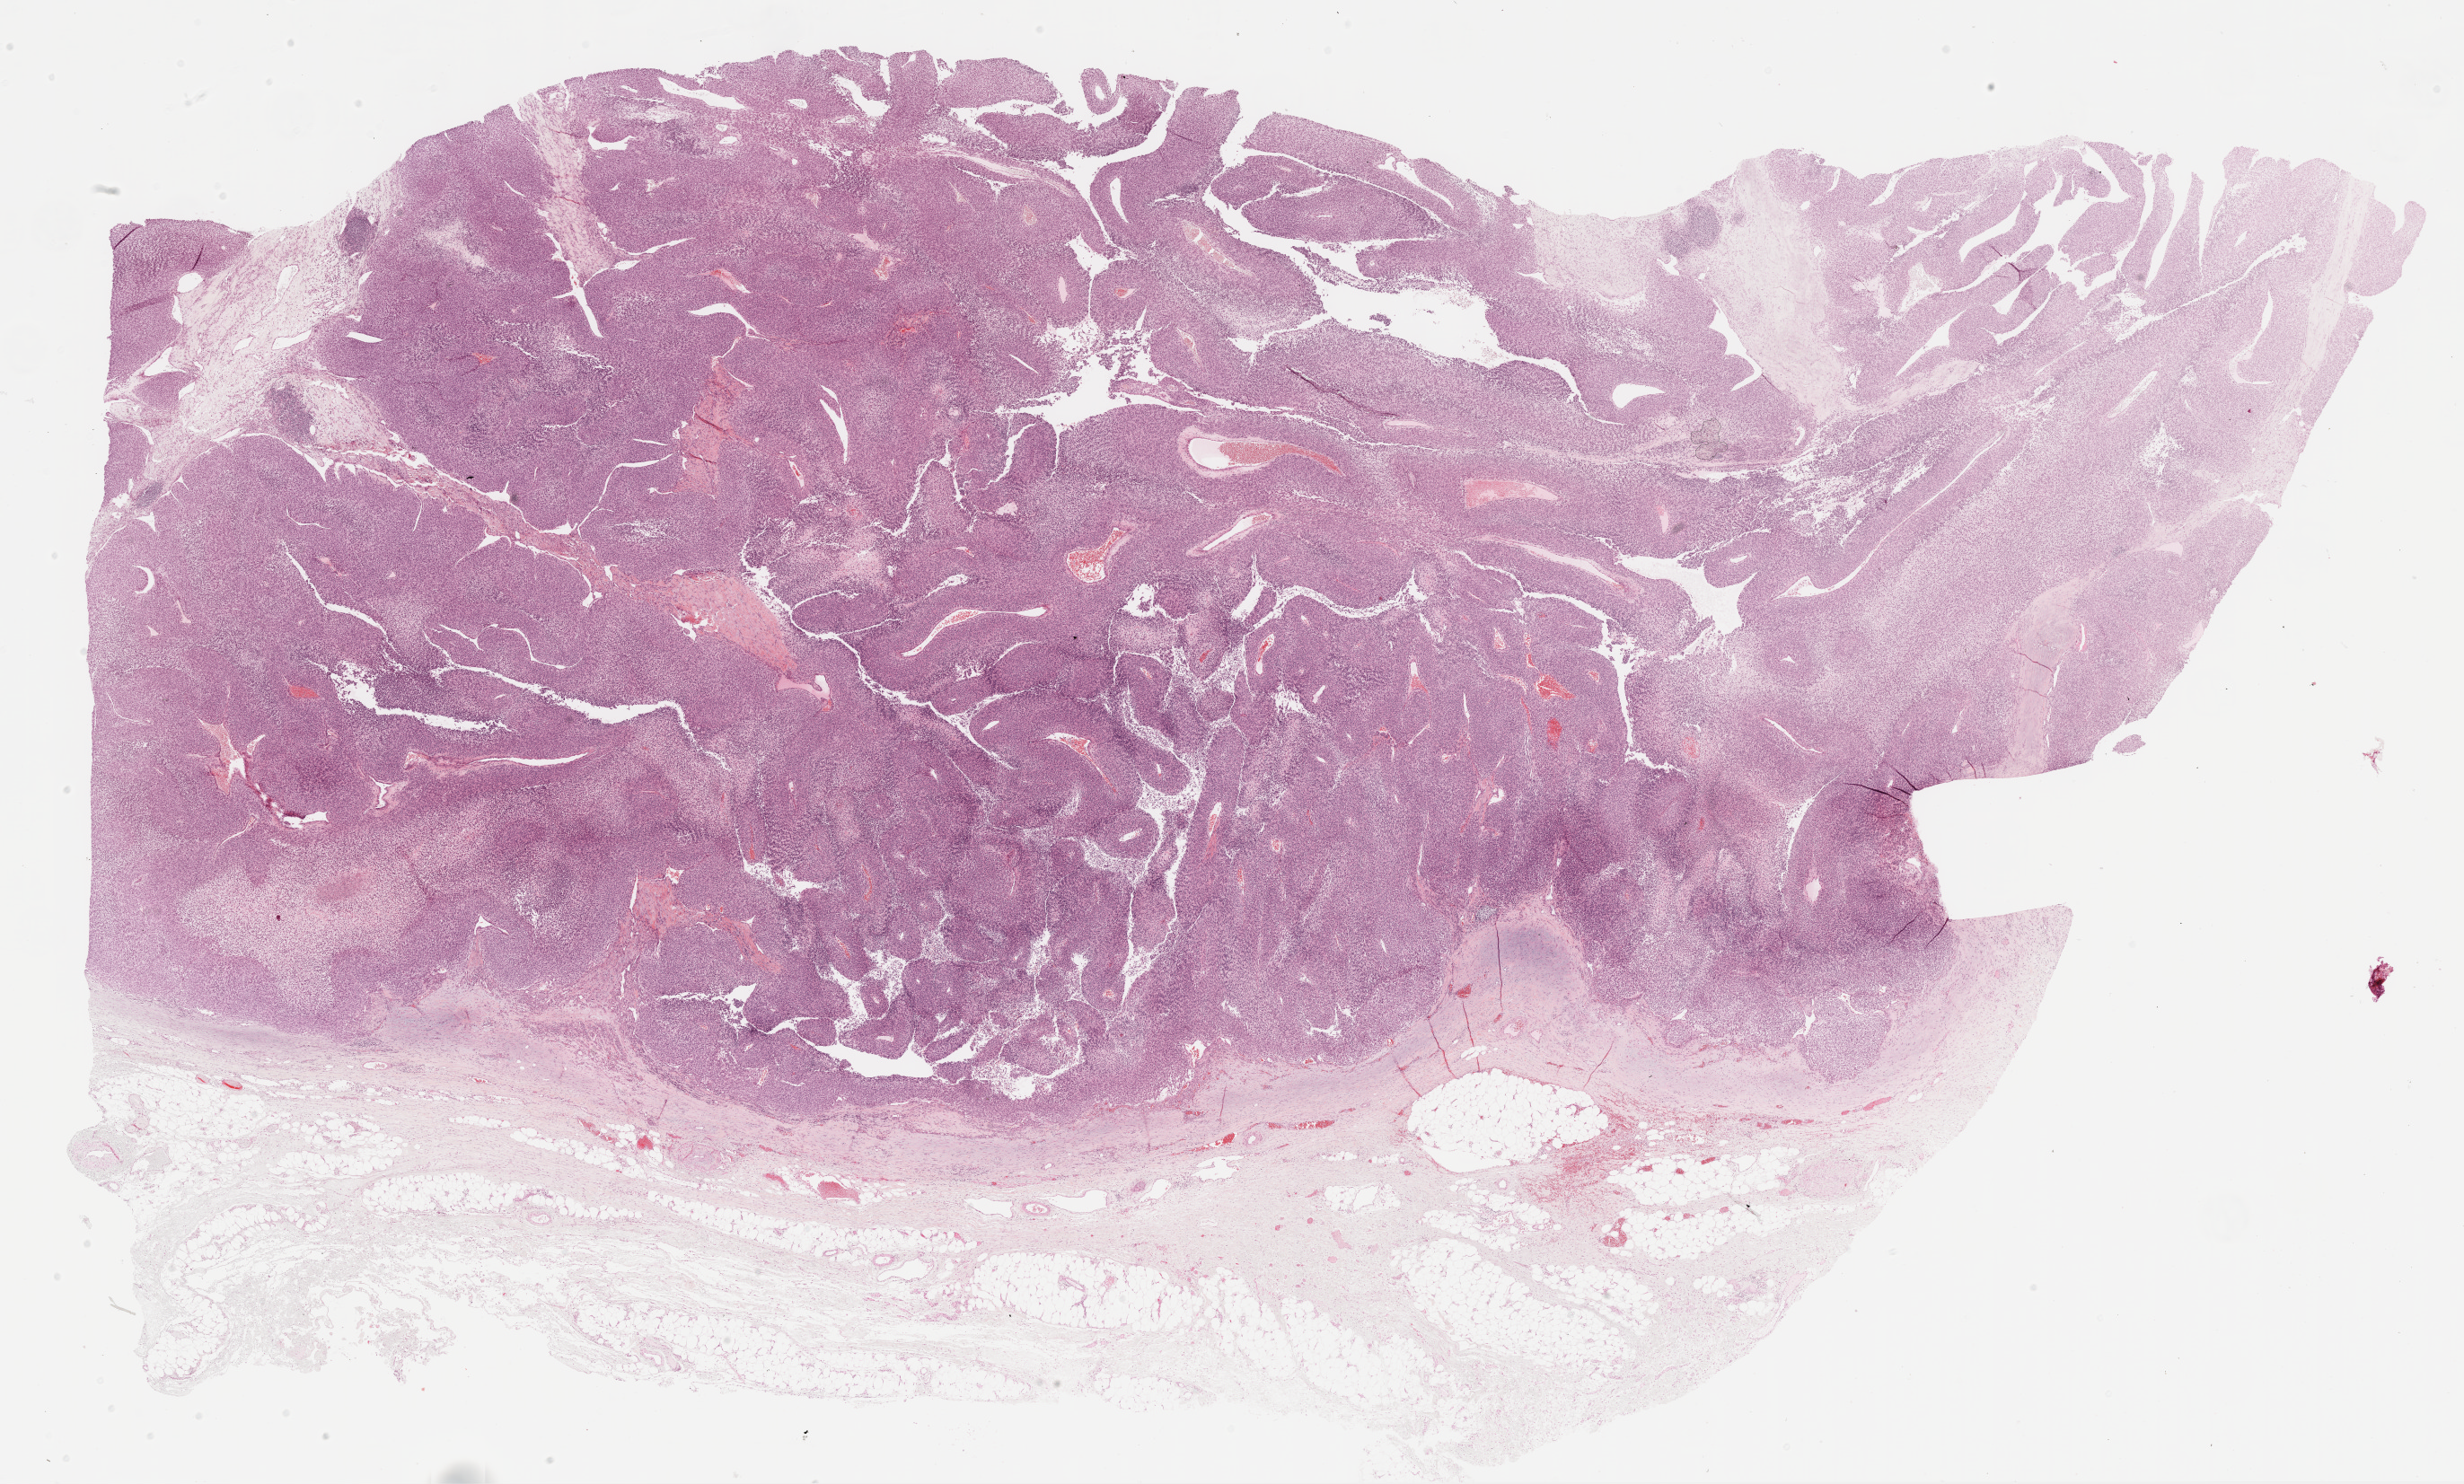
Digitized Hematoxylin and eosin (H&E) stained tissue section (whole slide) — a low-resolution overview of the entire scanned area, about 22.1 x 13.3 mm; formalin-fixed paraffin-embedded (FFPE) diagnostic section; metastatic tumour sample, sampled site: lymph node. Male, age 60 years at initial diagnosis.
This section: metastatic tumour tissue. Patient diagnosis: Malignant melanoma, NOS.